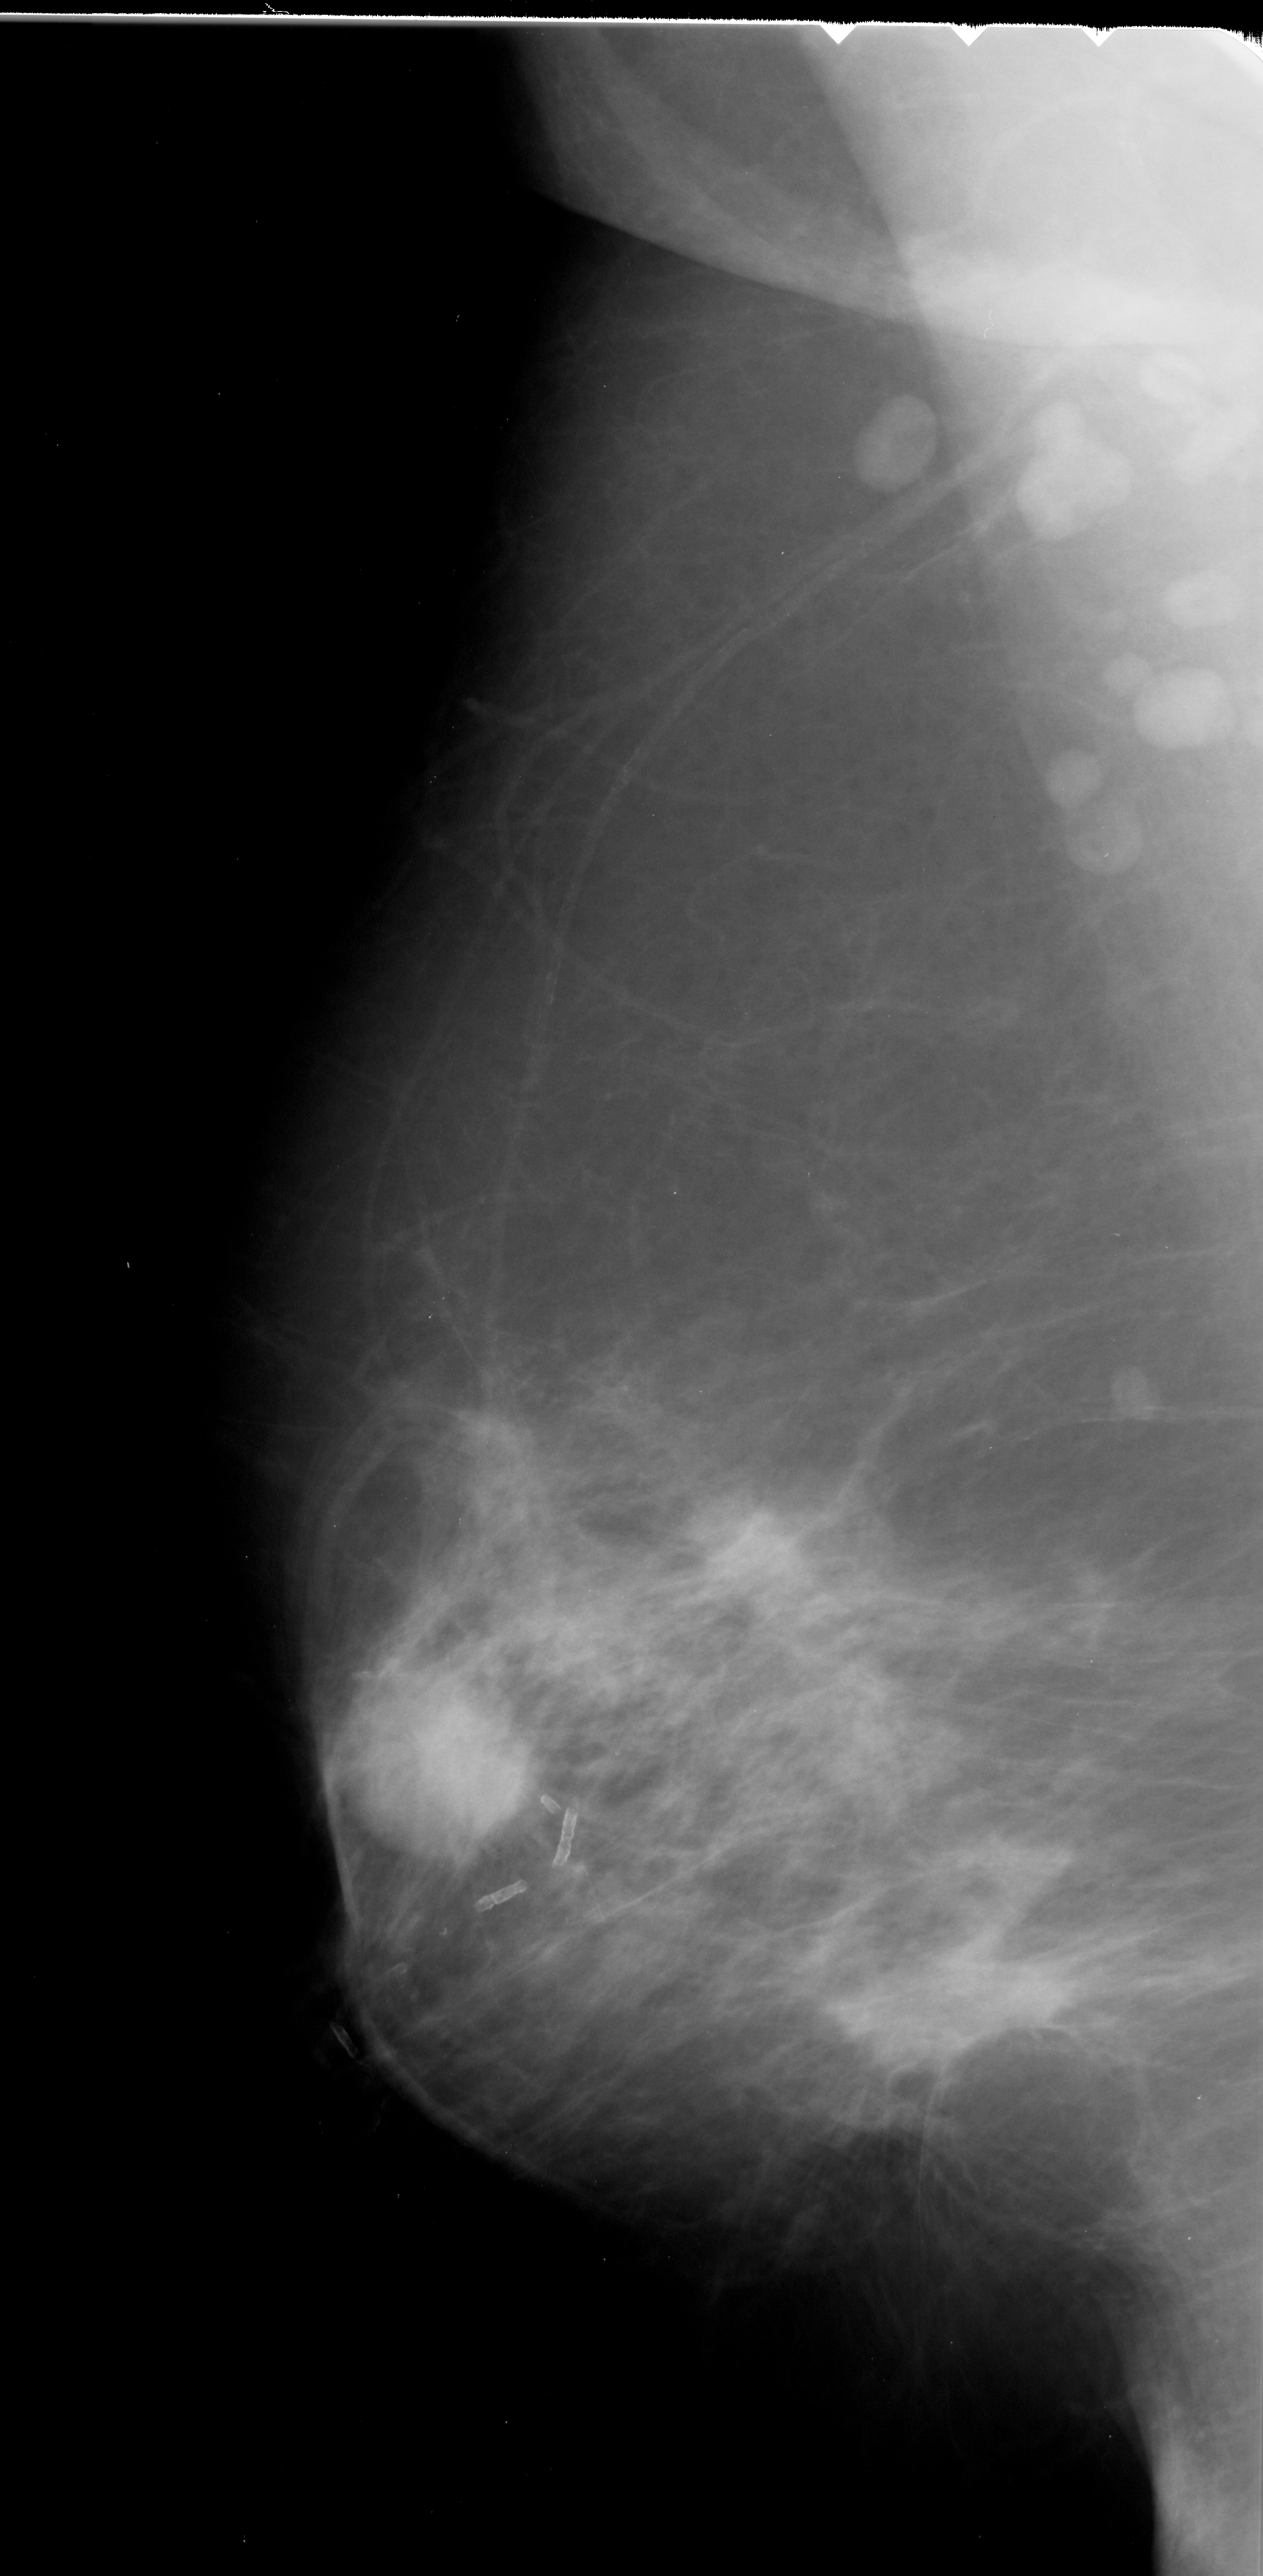
Scanned film-screen mammogram; left breast; MLO view; BI-RADS breast density category 2 (scale 1–4).
Abnormality record for this image: Finding 1 of 2: mass, shape round, margins spiculated; BI-RADS assessment category 5; pathology result (as recorded, not read from the image): malignant. Finding 2 of 2: mass, shape irregular, margins spiculated; BI-RADS assessment category 5; pathology result (as recorded, not read from the image): malignant.